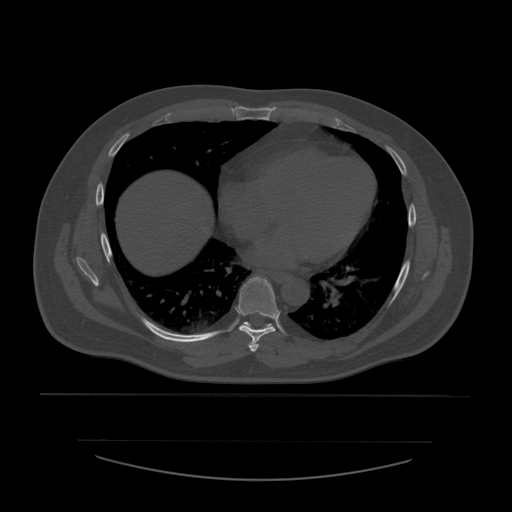
CT including the spine, one axial slice; slice 354 of 532 in the series (ordered by position); bone window (W 1800 / L 400 HU); 1.25 mm slice thickness; 512 × 512 image matrix, field of view 441 × 441 mm. Patient age 44 years. Case-level facts recorded for this patient, not image findings: primary cancer: soft tissue sarcoma.
Annotated regions visible in this slice (semi-automatic segmentation, software-assisted and operator-edited):
- T6 vertebra: bounding box [x1, y1, x2, y2] px = [248, 342, 259, 353]
- T7 vertebra: [239, 277, 281, 344]
- T8 vertebra: [245, 322, 273, 331]